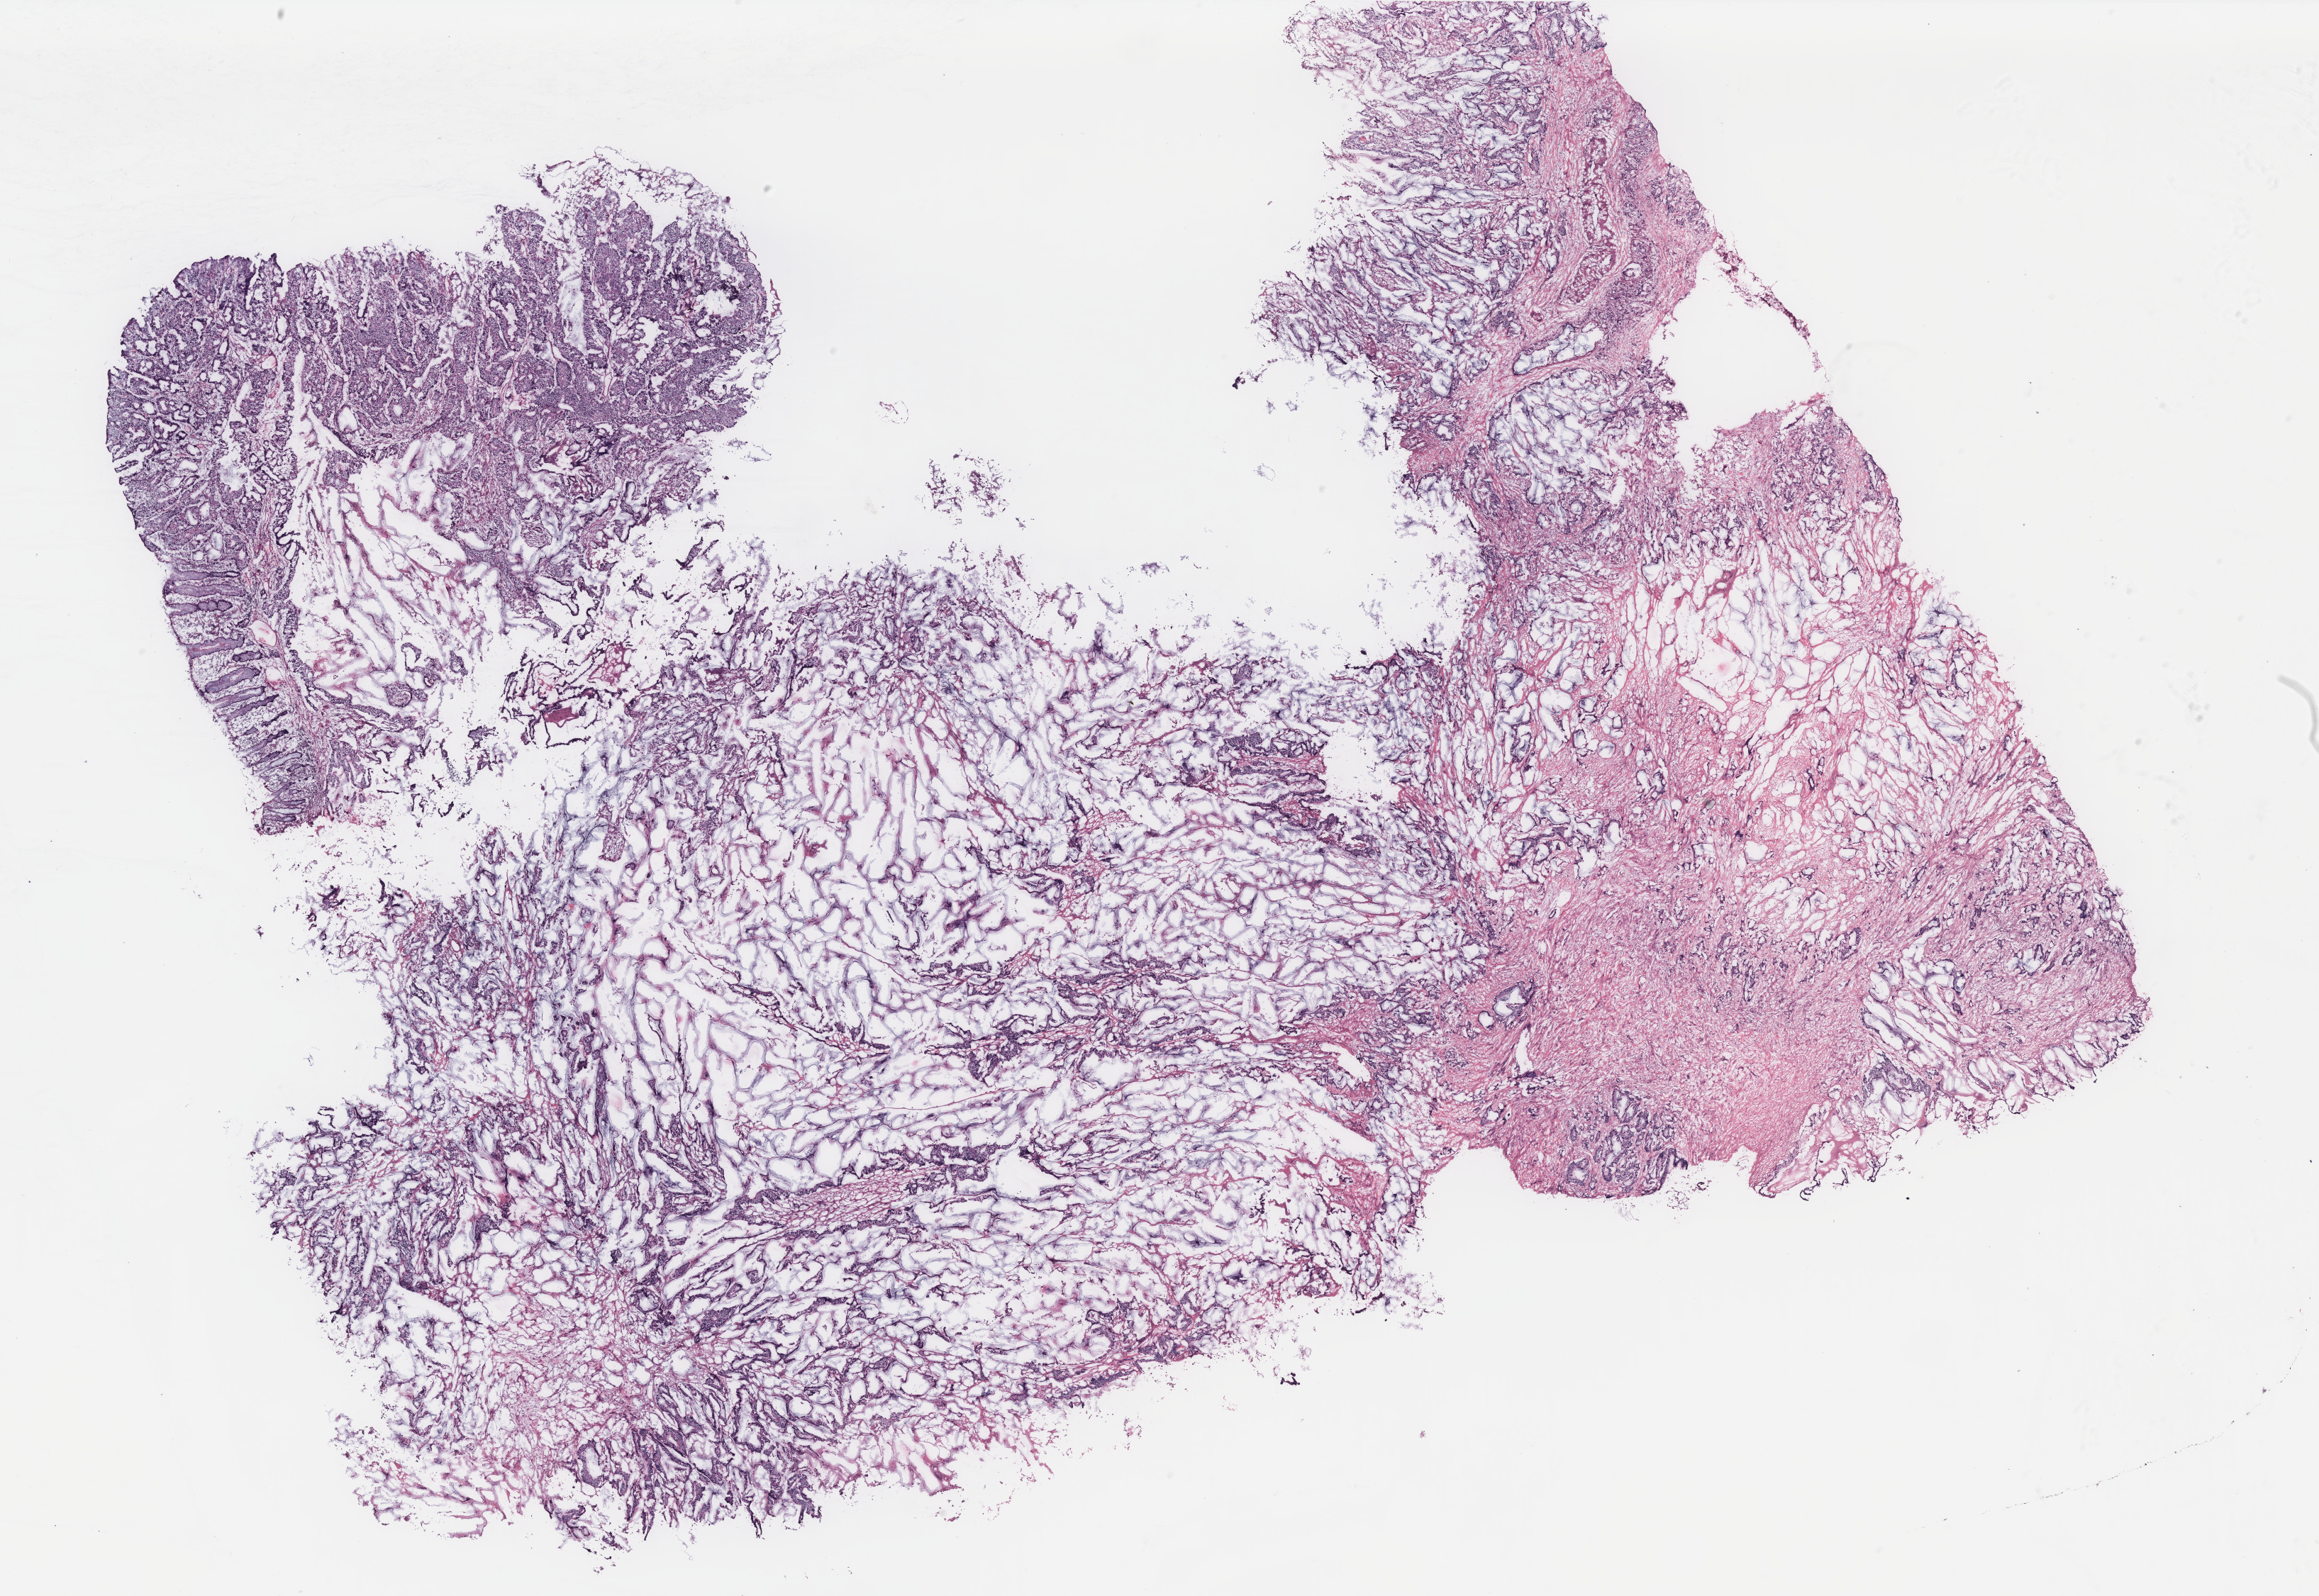
Digitized H&E-stained tissue section (whole slide), whole scanned area (about 26.2 x 18.0 mm, acquisition: 40x scan) shown as a low-resolution overview; colon, tissue type not recorded.
• patient diagnosis (cohort enrolment): colon cancer (colon)